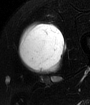
MRI of an extremity soft-tissue mass, one axial slice. T2-weighted fat-saturated. MR volume resampled by the dataset authors to the PET/CT grid (not the native acquisition matrix). 3.27 mm slice thickness. 90 × 105 image matrix. Male patient. Case-level facts recorded for this patient, not image findings: histological type: mixoid liposarcoma; grade: low; site of the primary tumour: left thigh.
Structures marked on this image (expert contour drawn on MRI and transferred to this co-registered scan by the dataset authors):
- gross tumour volume (mass): bounding box [x1, y1, x2, y2] px = [18, 23, 65, 76]